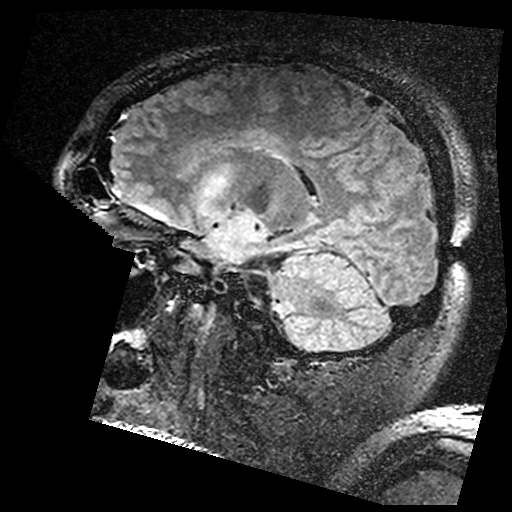
Brain MRI from a brain-tumour surgery series, one sagittal slice. Position 107 of 176 along the scan axis. T2 FLAIR. 512 × 512 image matrix, field of view 250 × 250 mm. From the clinical record (not read from this slice): histopathology: Astrocytoma; WHO grade: 3; IDH mutation: yes; tumour location: Left Insular.
Outlined on this slice (expert manual segmentation):
- residual tumour: bounding box [x1, y1, x2, y2] px = [204, 169, 234, 198]